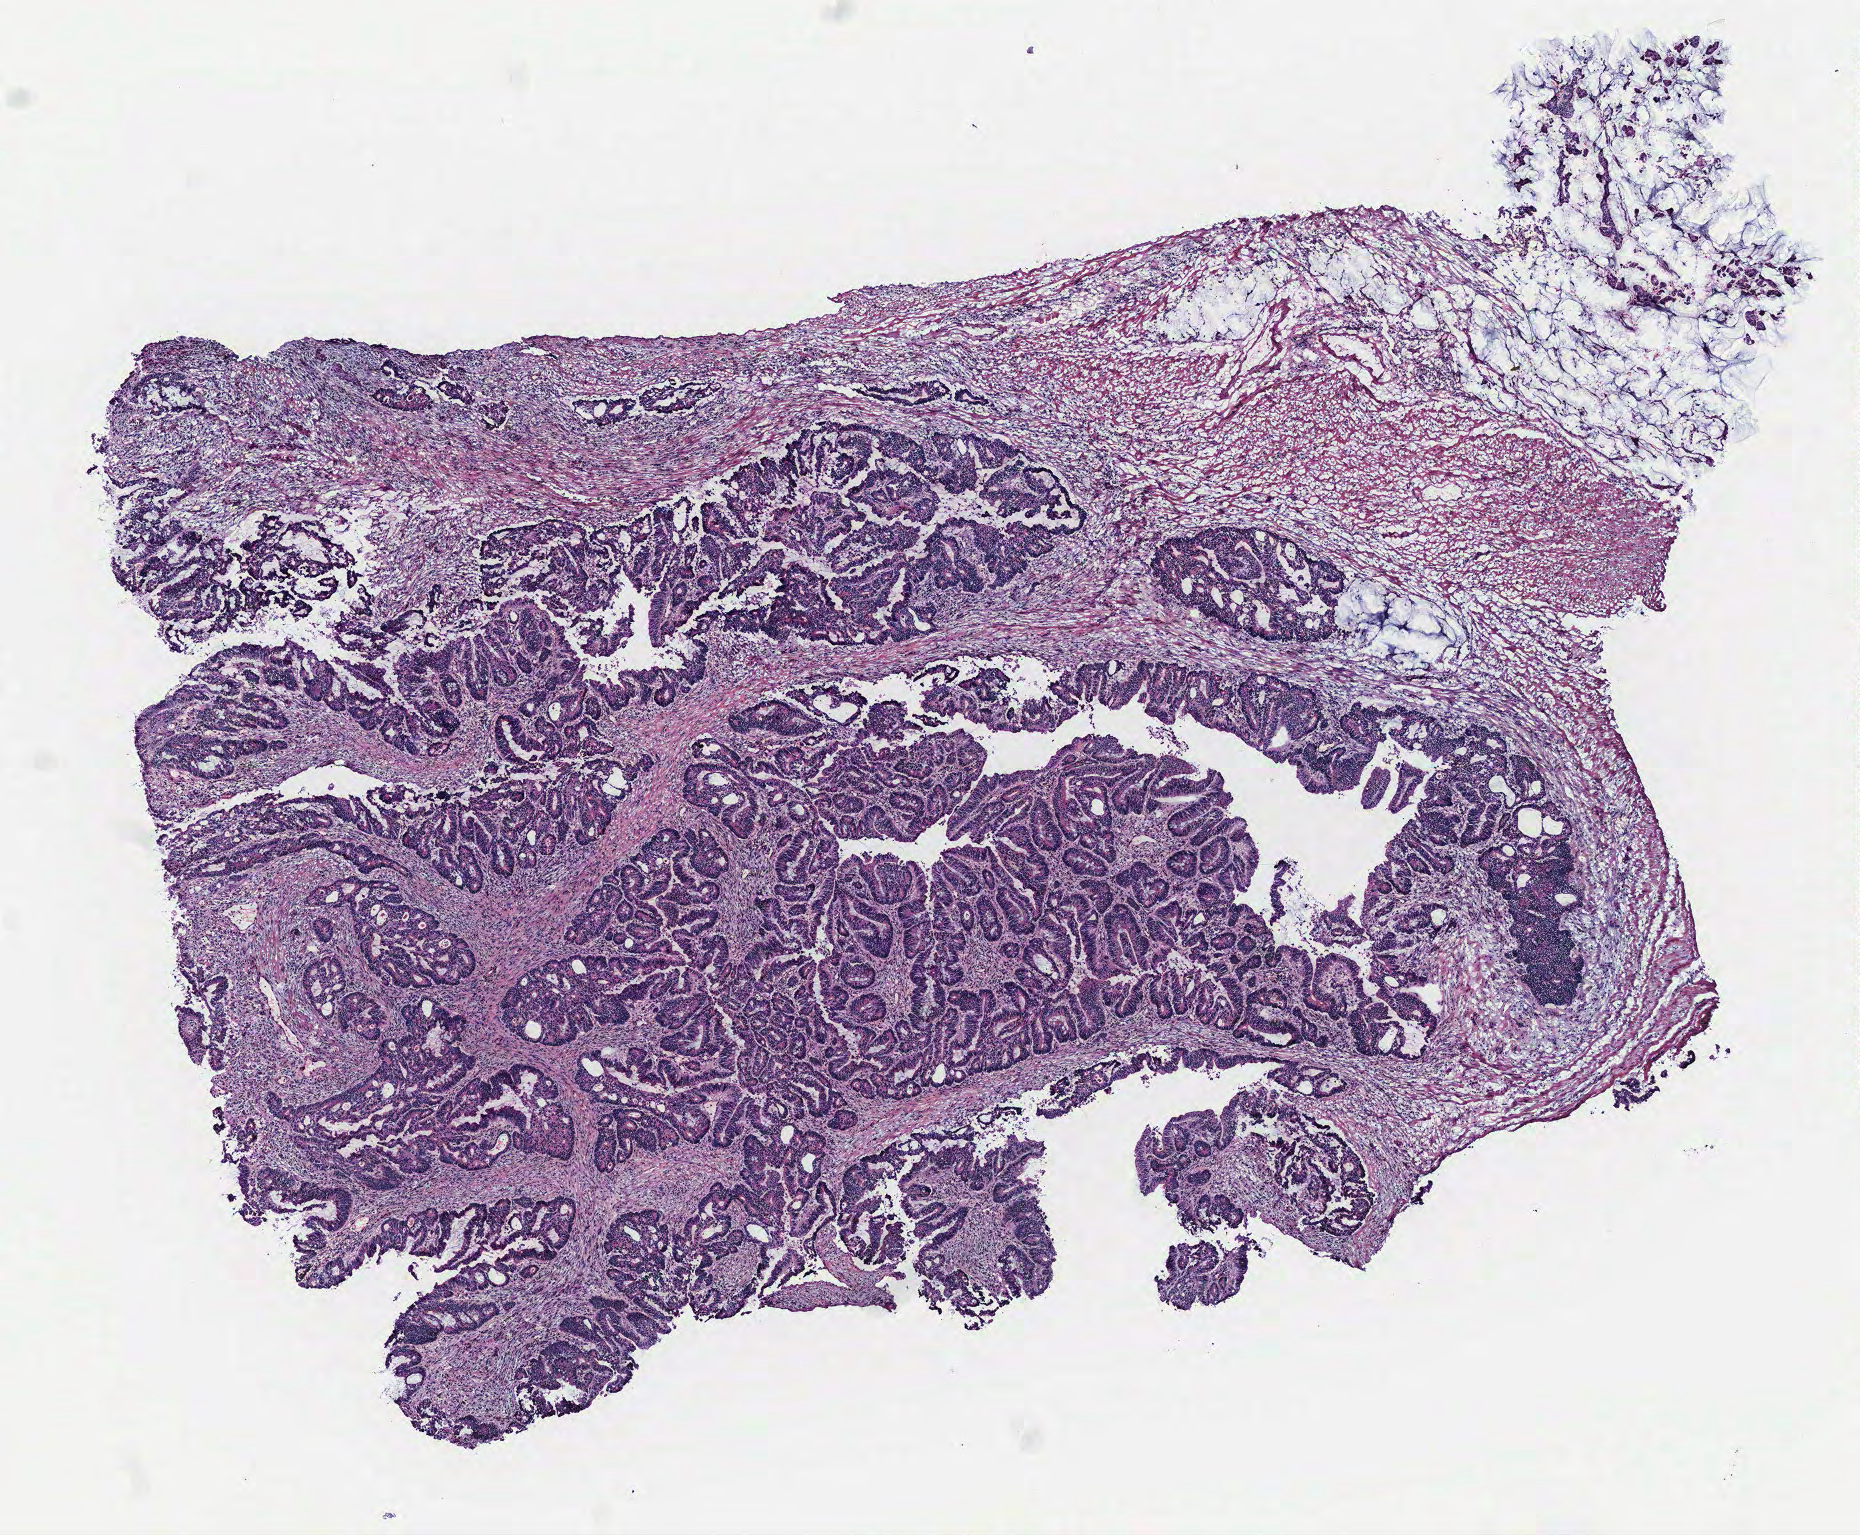
Digitized H&E tissue section (whole slide), shown as a low-resolution overview of the whole scanned area (about 7.4 x 6.1 mm, slide scanned at 40x). Tumour tissue sample, colon. Patient: female, age 69 years.
AJCC pathologic stage: IIIB. Primary tumour site (as recorded): colon. Diagnosis: Adenocarcinoma, NOS.